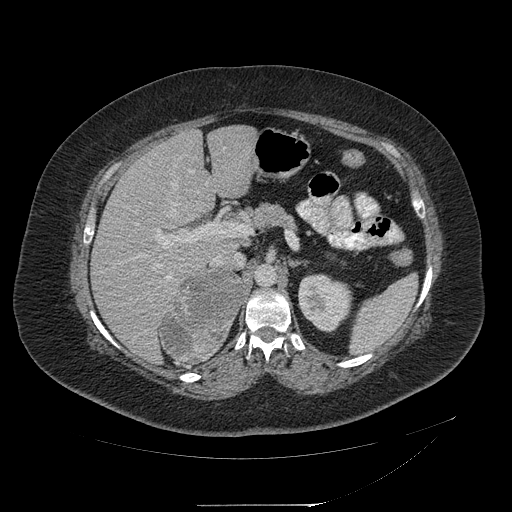
Contrast-enhanced abdominal CT, one axial slice; slice 132 of 217 in the series (ordered by position); 120 kVp; intravenous contrast given; soft-tissue window (W 400 / L 40 HU); 1.25 mm slice thickness; 512 × 512 image matrix, field of view 453 × 453 mm. Female patient, age 55 years. Case-level facts recorded for this patient, not image findings: diagnosis: adrenocortical carcinoma; tumour side: right adrenal; tumour size at pathology: 11 cm.
Annotated regions visible in this slice (semi-automatically segmented with operator editing):
- mass: bounding box [x1, y1, x2, y2] px = [162, 272, 243, 362]